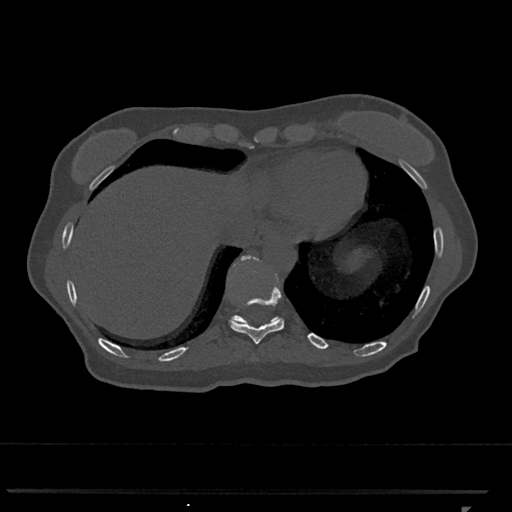
CT including the spine, one axial slice; position 559 of 793 along the scan axis; reconstruction kernel Br40s/3; bone window (W 1800 / L 400 HU); 512 × 512 image matrix, field of view 380 × 380 mm. Patient: female, 62 years. Case-level facts recorded for this patient, not image findings: primary cancer: renal.
Structures marked on this image (semi-automatically segmented with operator editing):
- T10 vertebra: box from (x=229, y=269) to (x=284, y=344) px
- T11 vertebra: (x=229, y=255)–(x=281, y=324)